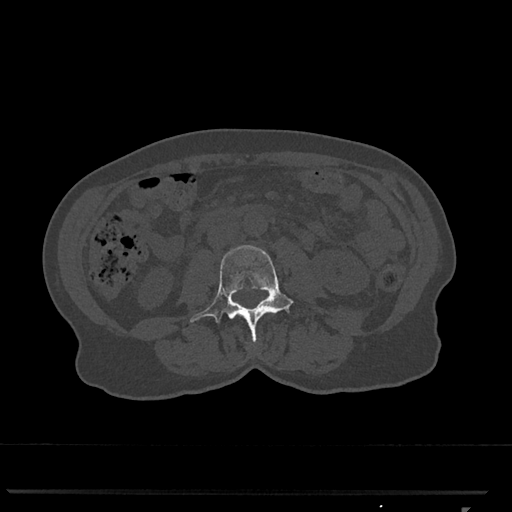
CT including the spine, one axial slice; slice 275 of 793 in the series (ordered by position); reconstruction kernel Br40s/3; 120 kVp; bone window (W 1800 / L 400 HU); 512 × 512 image matrix. Patient: female, 62 years. From the clinical record (not read from this slice): primary cancer: renal.
Outlined on this slice (semi-automatically segmented with operator editing):
- L3 vertebra: bounding box [x1, y1, x2, y2] px = [190, 245, 294, 343]